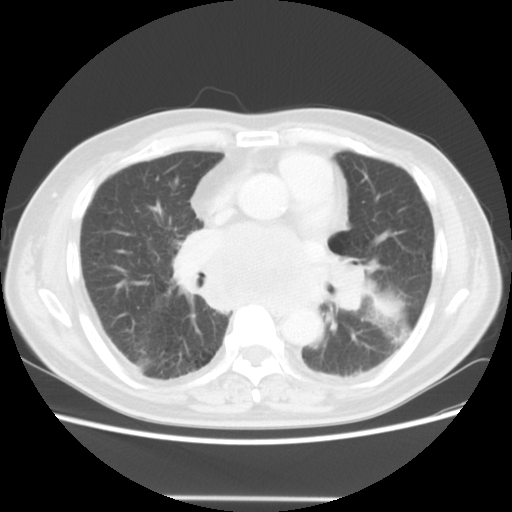
Chest CT, one axial slice. 140 kVp. Lung window (W 1500 / L -600 HU). 512 × 512 image matrix, field of view 360 × 360 mm. Patient: male, 66 years. From the clinical record (not read from this slice): clinical TNM (as recorded): T4 N3 M0.
Outlined on this slice (rectangle marked by the reading radiologist):
- lung tumour (recorded histology: small cell carcinoma): box from (x=373, y=288) to (x=408, y=331) px